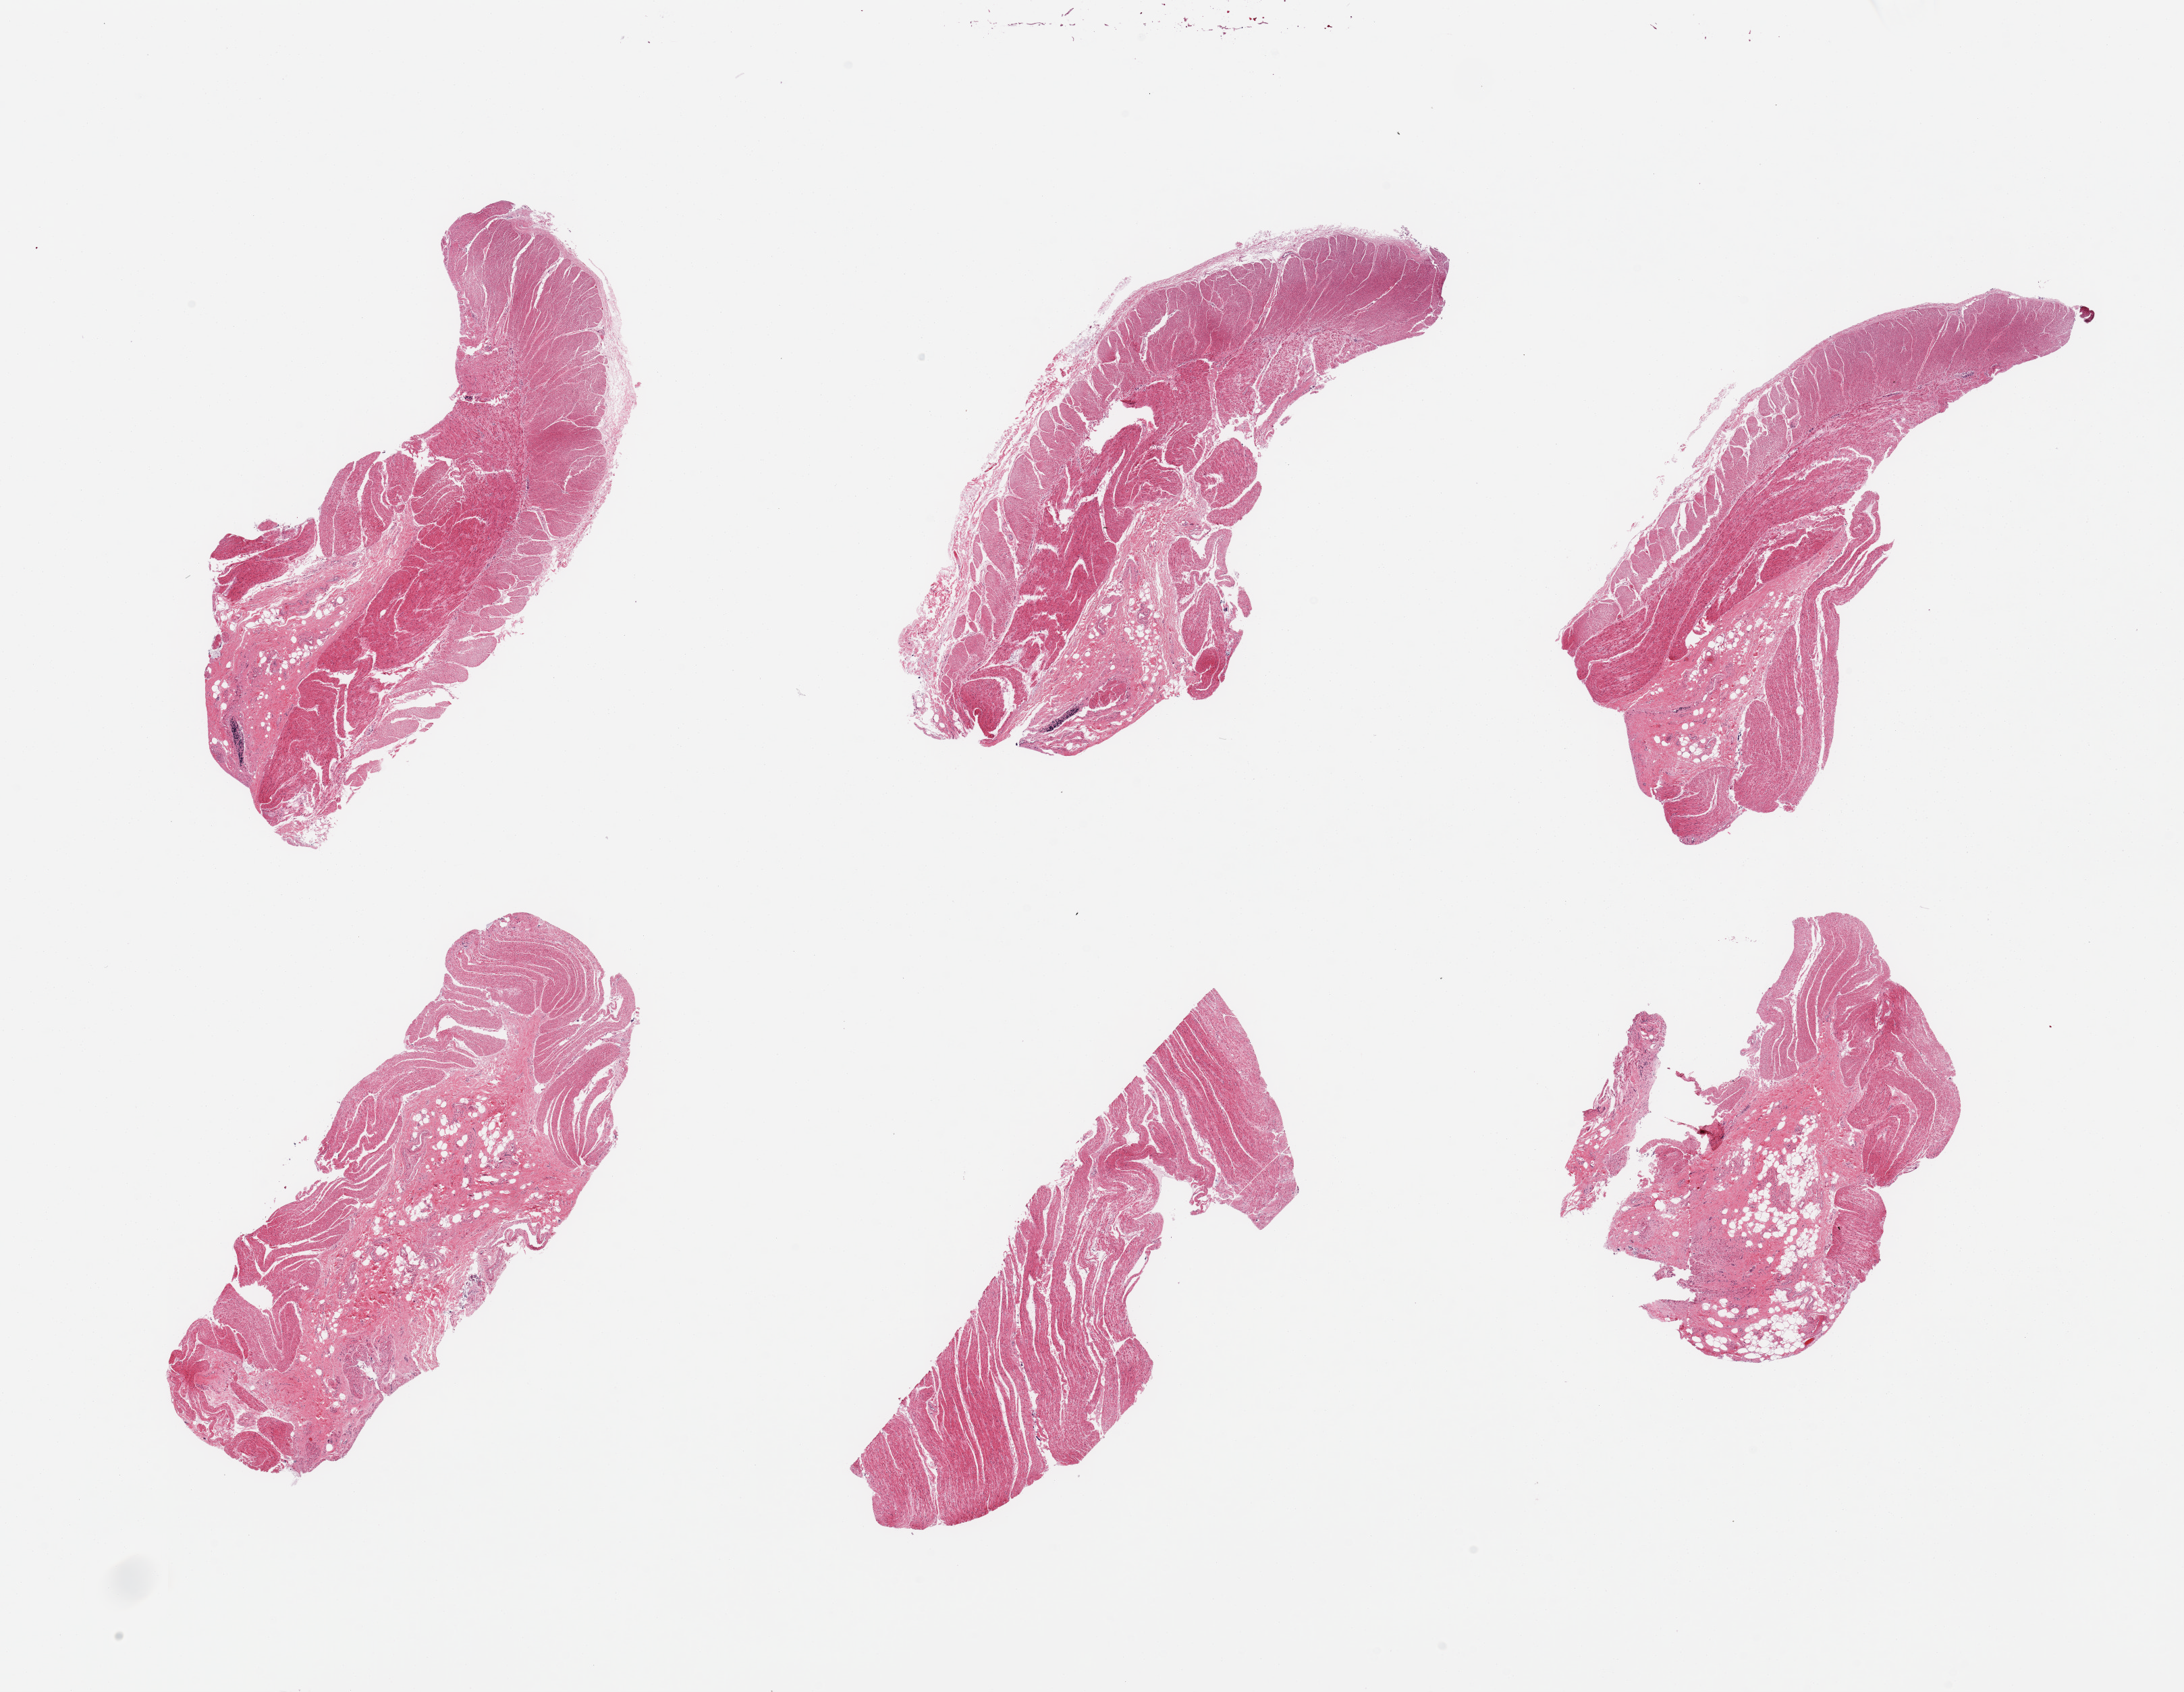
Digitized haematoxylin and eosin-stained section, a low-resolution overview of the entire scanned area, about 25.6 x 19.8 mm (from a 20x scan). PAXgene-fixed paraffin-embedded (PFPE) section. Section of sigmoid colon (target tissue). Tissue donor sample. Donor sex: male.
• review note (as recorded): 6 pieces; well dissected muscularis, but not well preserved